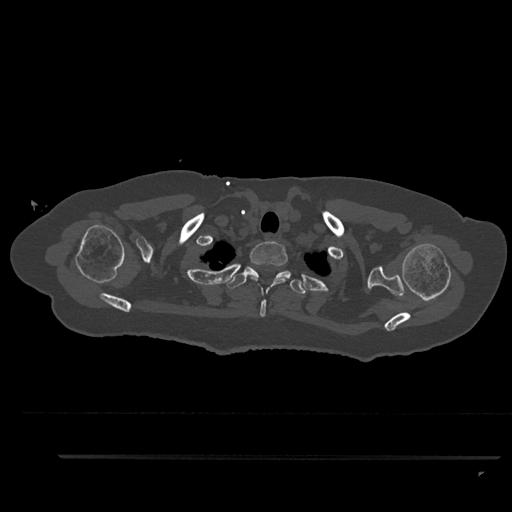
CT including the spine, one axial slice. Position 743 of 797 along the scan axis. Reconstruction kernel Br40s/3. 120 kVp. Bone window (W 1800 / L 400 HU). 0.5 mm slice thickness. 512 × 512 image matrix, field of view 408 × 408 mm. Patient: female, 44 years. From the clinical record (not read from this slice): primary cancer: renal.
Structures marked on this image (semi-automatic segmentation, software-assisted and operator-edited):
- T1 vertebra: bounding box (x1, y1, x2, y2) in pixels: (248, 241, 288, 317)
- T2 vertebra: (226, 266, 306, 294)